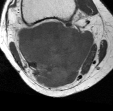
MRI of an extremity soft-tissue mass, one axial slice; position 25 of 45 along the scan axis; MR volume resampled by the dataset authors to the PET/CT grid (not the native acquisition matrix); 3.27 mm slice thickness; 113 × 111 image matrix, field of view 110 × 108 mm. Female patient. Case-level facts recorded for this patient, not image findings: histological type: liposarcoma; site of the primary tumour: right thigh.
Structures marked on this image (expert contour drawn on MRI and transferred to this co-registered scan by the dataset authors):
- gross tumour volume (mass): bounding box <17,21,95,88> (left, top, right, bottom; pixels)